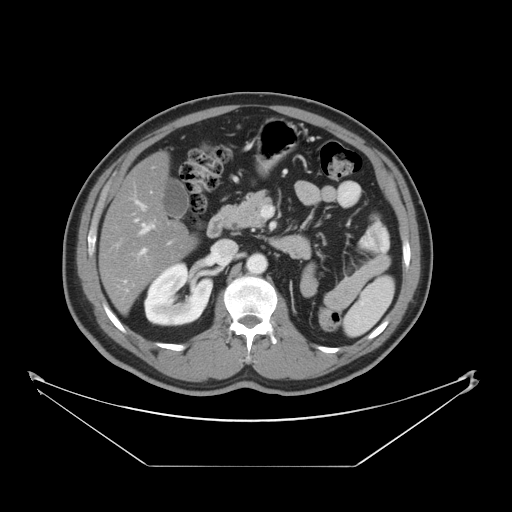
Contrast-enhanced abdominal CT, one axial slice. Slice 21 of 46 in the series (ordered by position). Soft-tissue window (W 400 / L 40 HU). 5 mm slice thickness. 512 × 512 image matrix. Male patient, age 57 years. From the clinical record (not read from this slice): diagnosis: colorectal cancer liver metastases, imaged before liver resection; multiple liver metastases: no.
Outlined on this slice (manually delineated by an expert):
- hepatic veins: bounding box (x1, y1, x2, y2) in pixels: (135, 219, 149, 232)
- liver: (101, 154, 194, 311)
- planned liver remnant (the part of the liver to remain after resection): (101, 154, 194, 311)
- portal vein (with intrahepatic branches): (141, 204, 146, 253)